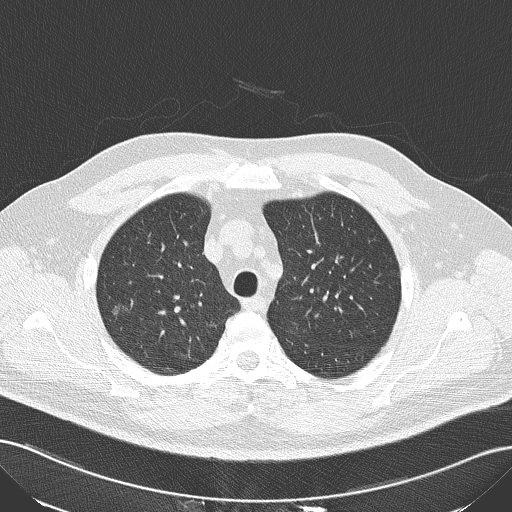
Low-dose screening chest CT, one axial slice. Reconstruction kernel B50f. 120 kVp. Lung window (W 1500 / L -600 HU). 2 mm slice thickness. 512 × 512 image matrix, field of view 360 × 360 mm.
Outlined on this slice (manually delineated by an expert):
- lesion 1 (tumor, upper lobe of right lung): bounding box <112,302,130,315> (left, top, right, bottom; pixels)